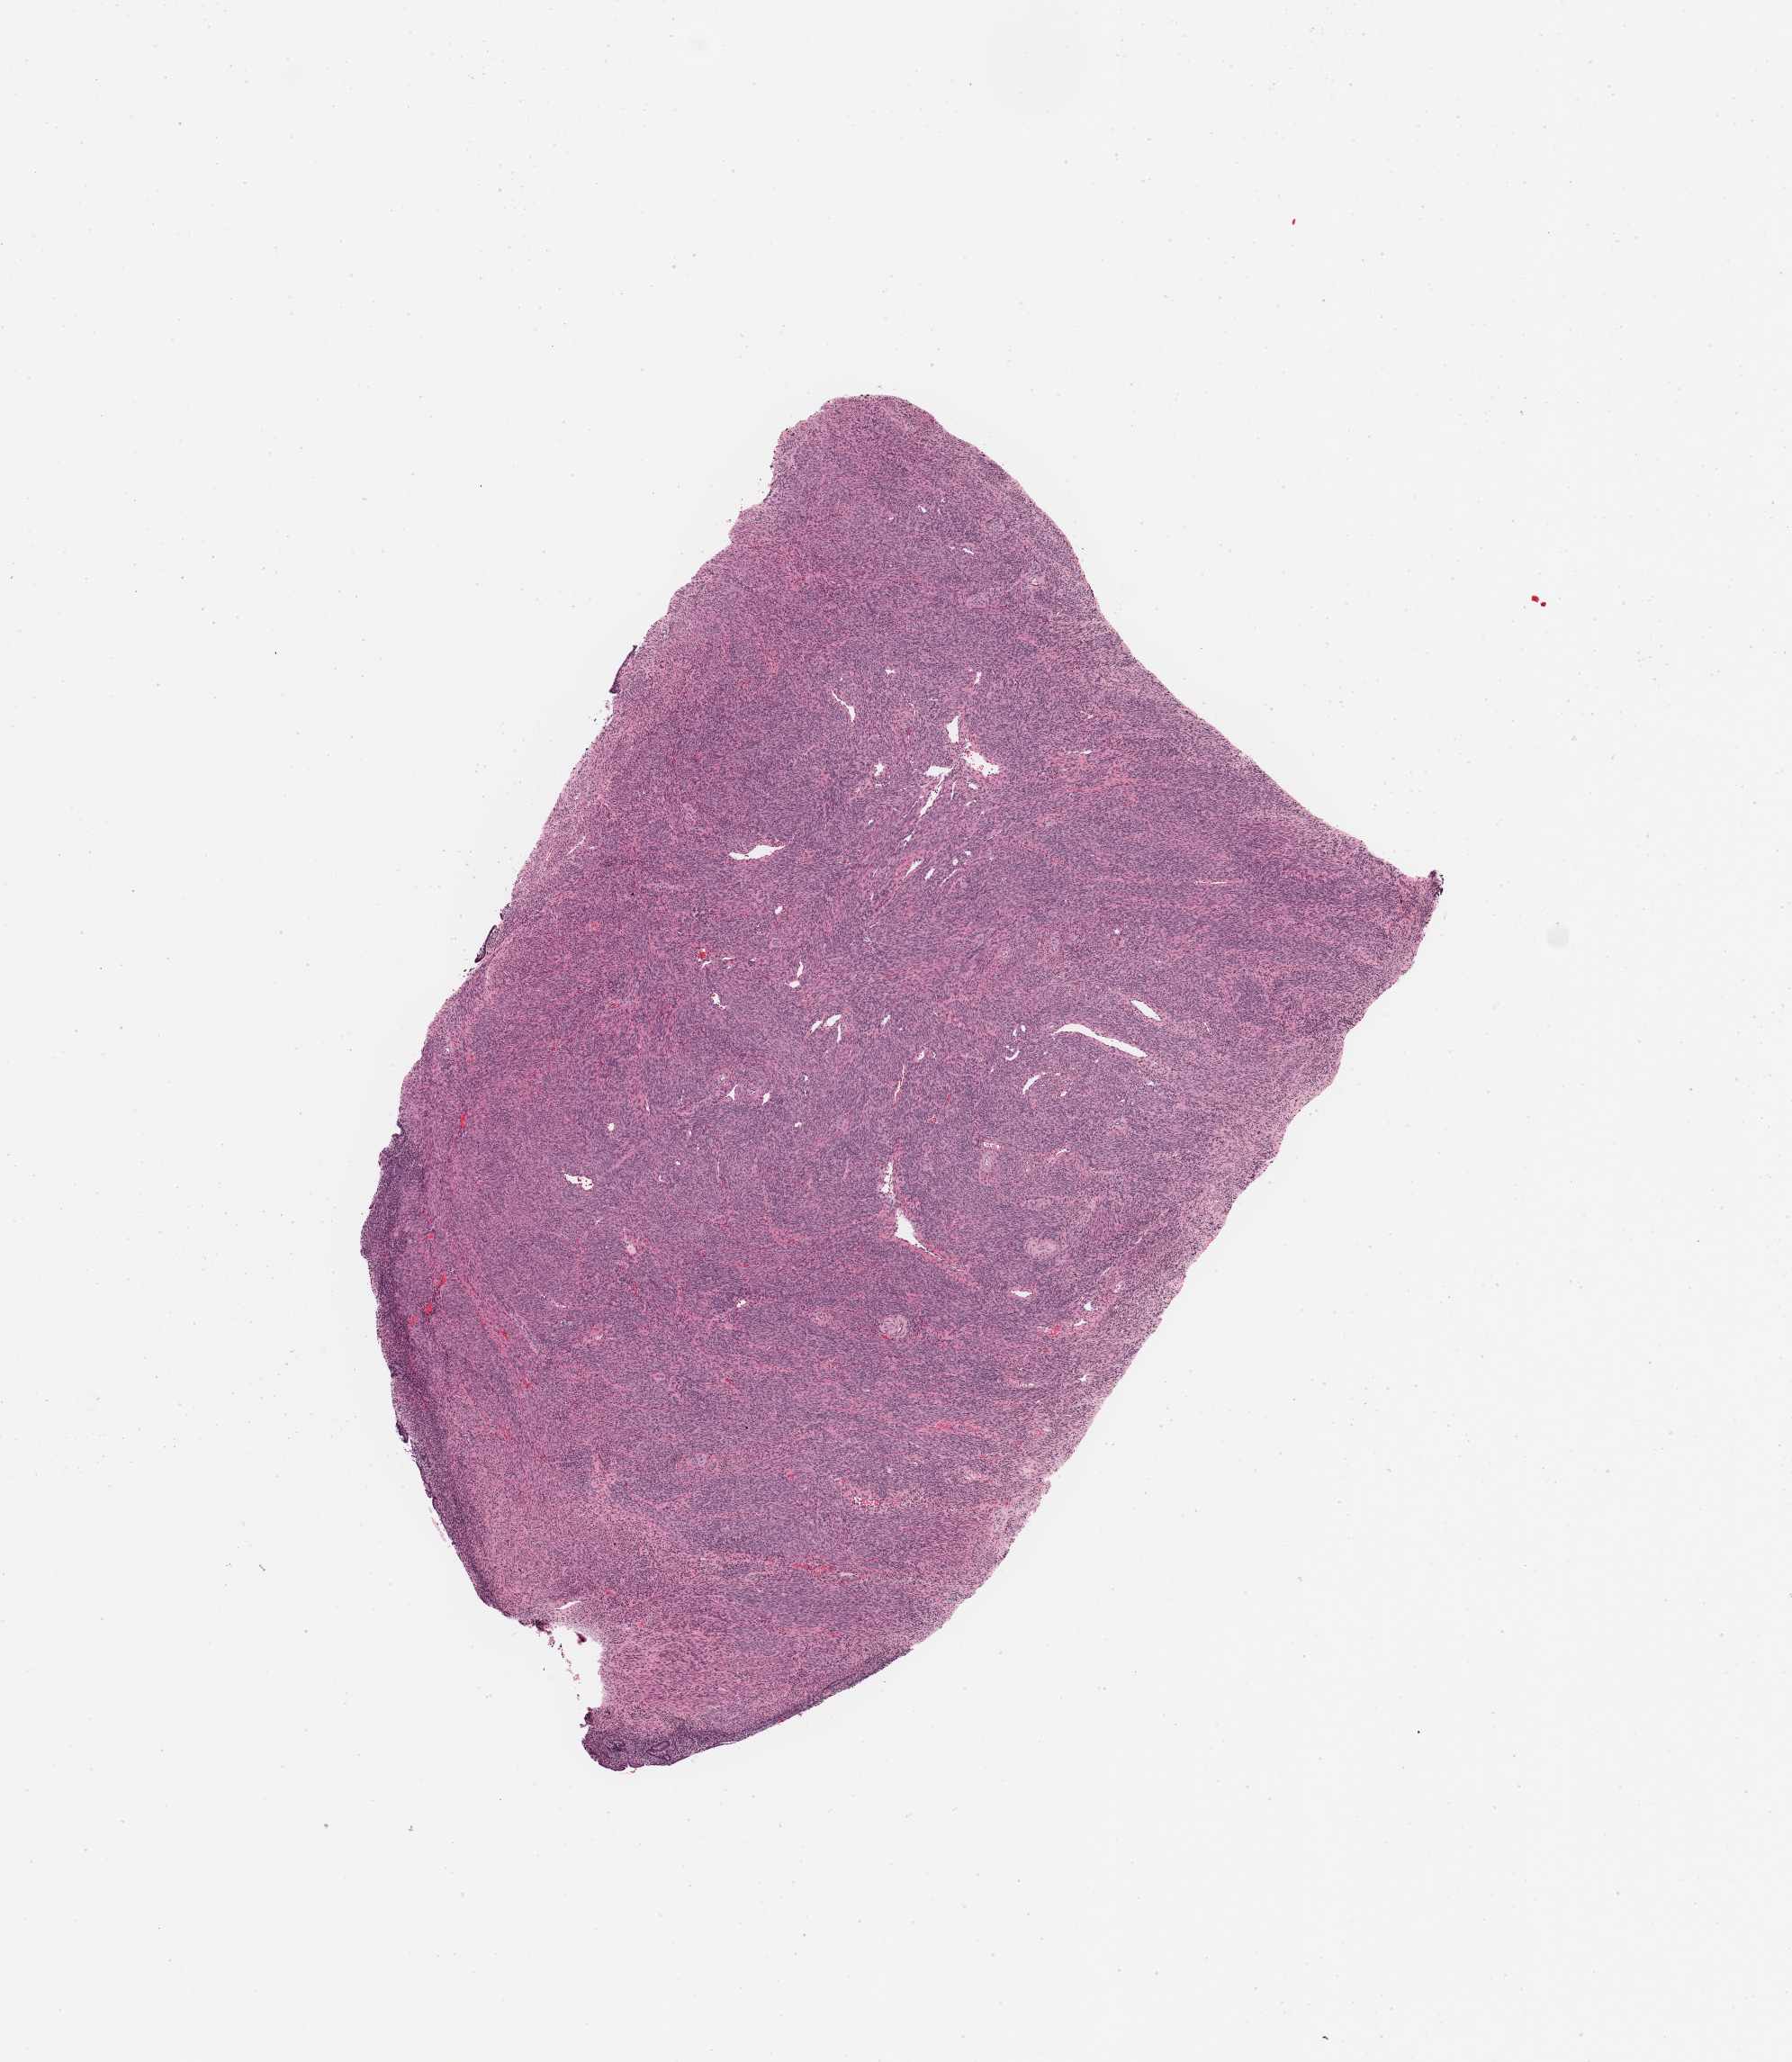
Whole-slide histology image, Hematoxylin and eosin (H&E) stained — low-resolution overview of the scanned area, about 7.9 x 9.1 mm (slide scanned at 20x). Uterus, tissue type not recorded.
Patient diagnosis (cohort enrolment): corpus endometrial carcinoma (uterus).